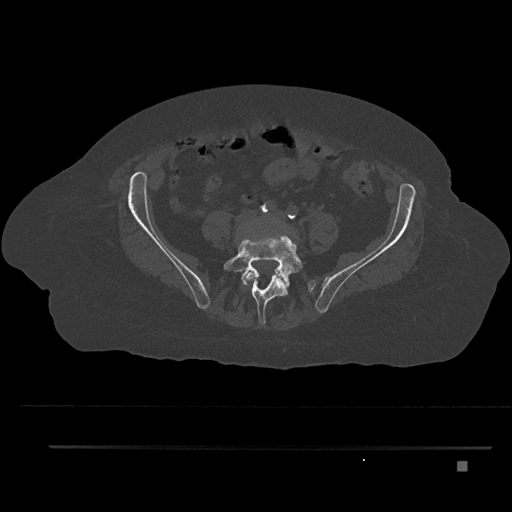
CT including the spine, one axial slice; position 44 of 797 along the scan axis; reconstruction kernel Br40s/3; 120 kVp; bone window (W 1800 / L 400 HU); 0.5 mm slice thickness; 512 × 512 image matrix. Patient: female, 76 years. From the clinical record (not read from this slice): primary cancer: lung; vertebrae with lytic lesions (as recorded): T11, L3.
Annotated regions visible in this slice (semi-automatic segmentation, software-assisted and operator-edited):
- L4 vertebra: bounding box <244,268,287,302> (left, top, right, bottom; pixels)
- L5 vertebra: <223,226,304,325>